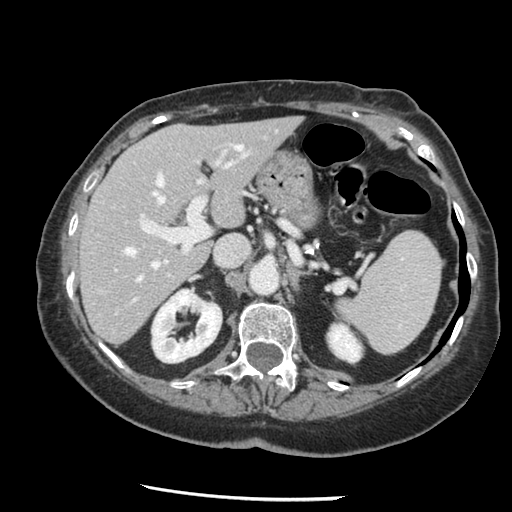
Contrast-enhanced abdominal CT, one axial slice; position 84 of 148 along the scan axis; reconstruction kernel STANDARD; intravenous contrast given; soft-tissue window (W 400 / L 40 HU); 2.5 mm slice thickness; 512 × 512 image matrix, field of view 330 × 330 mm. Female patient, age 85 years. From the clinical record (not read from this slice): diagnosis: colorectal cancer liver metastases, imaged before liver resection; multiple liver metastases: no; largest metastasis: 0.9 cm; disease in both lobes: no.
Annotated regions visible in this slice (outlined manually by an expert reader):
- hepatic veins: bounding box (x1, y1, x2, y2) in pixels: (125, 146, 241, 281)
- liver: (81, 118, 300, 343)
- planned liver remnant (the part of the liver to remain after resection): (81, 118, 300, 343)
- portal vein (with intrahepatic branches): (142, 142, 231, 251)